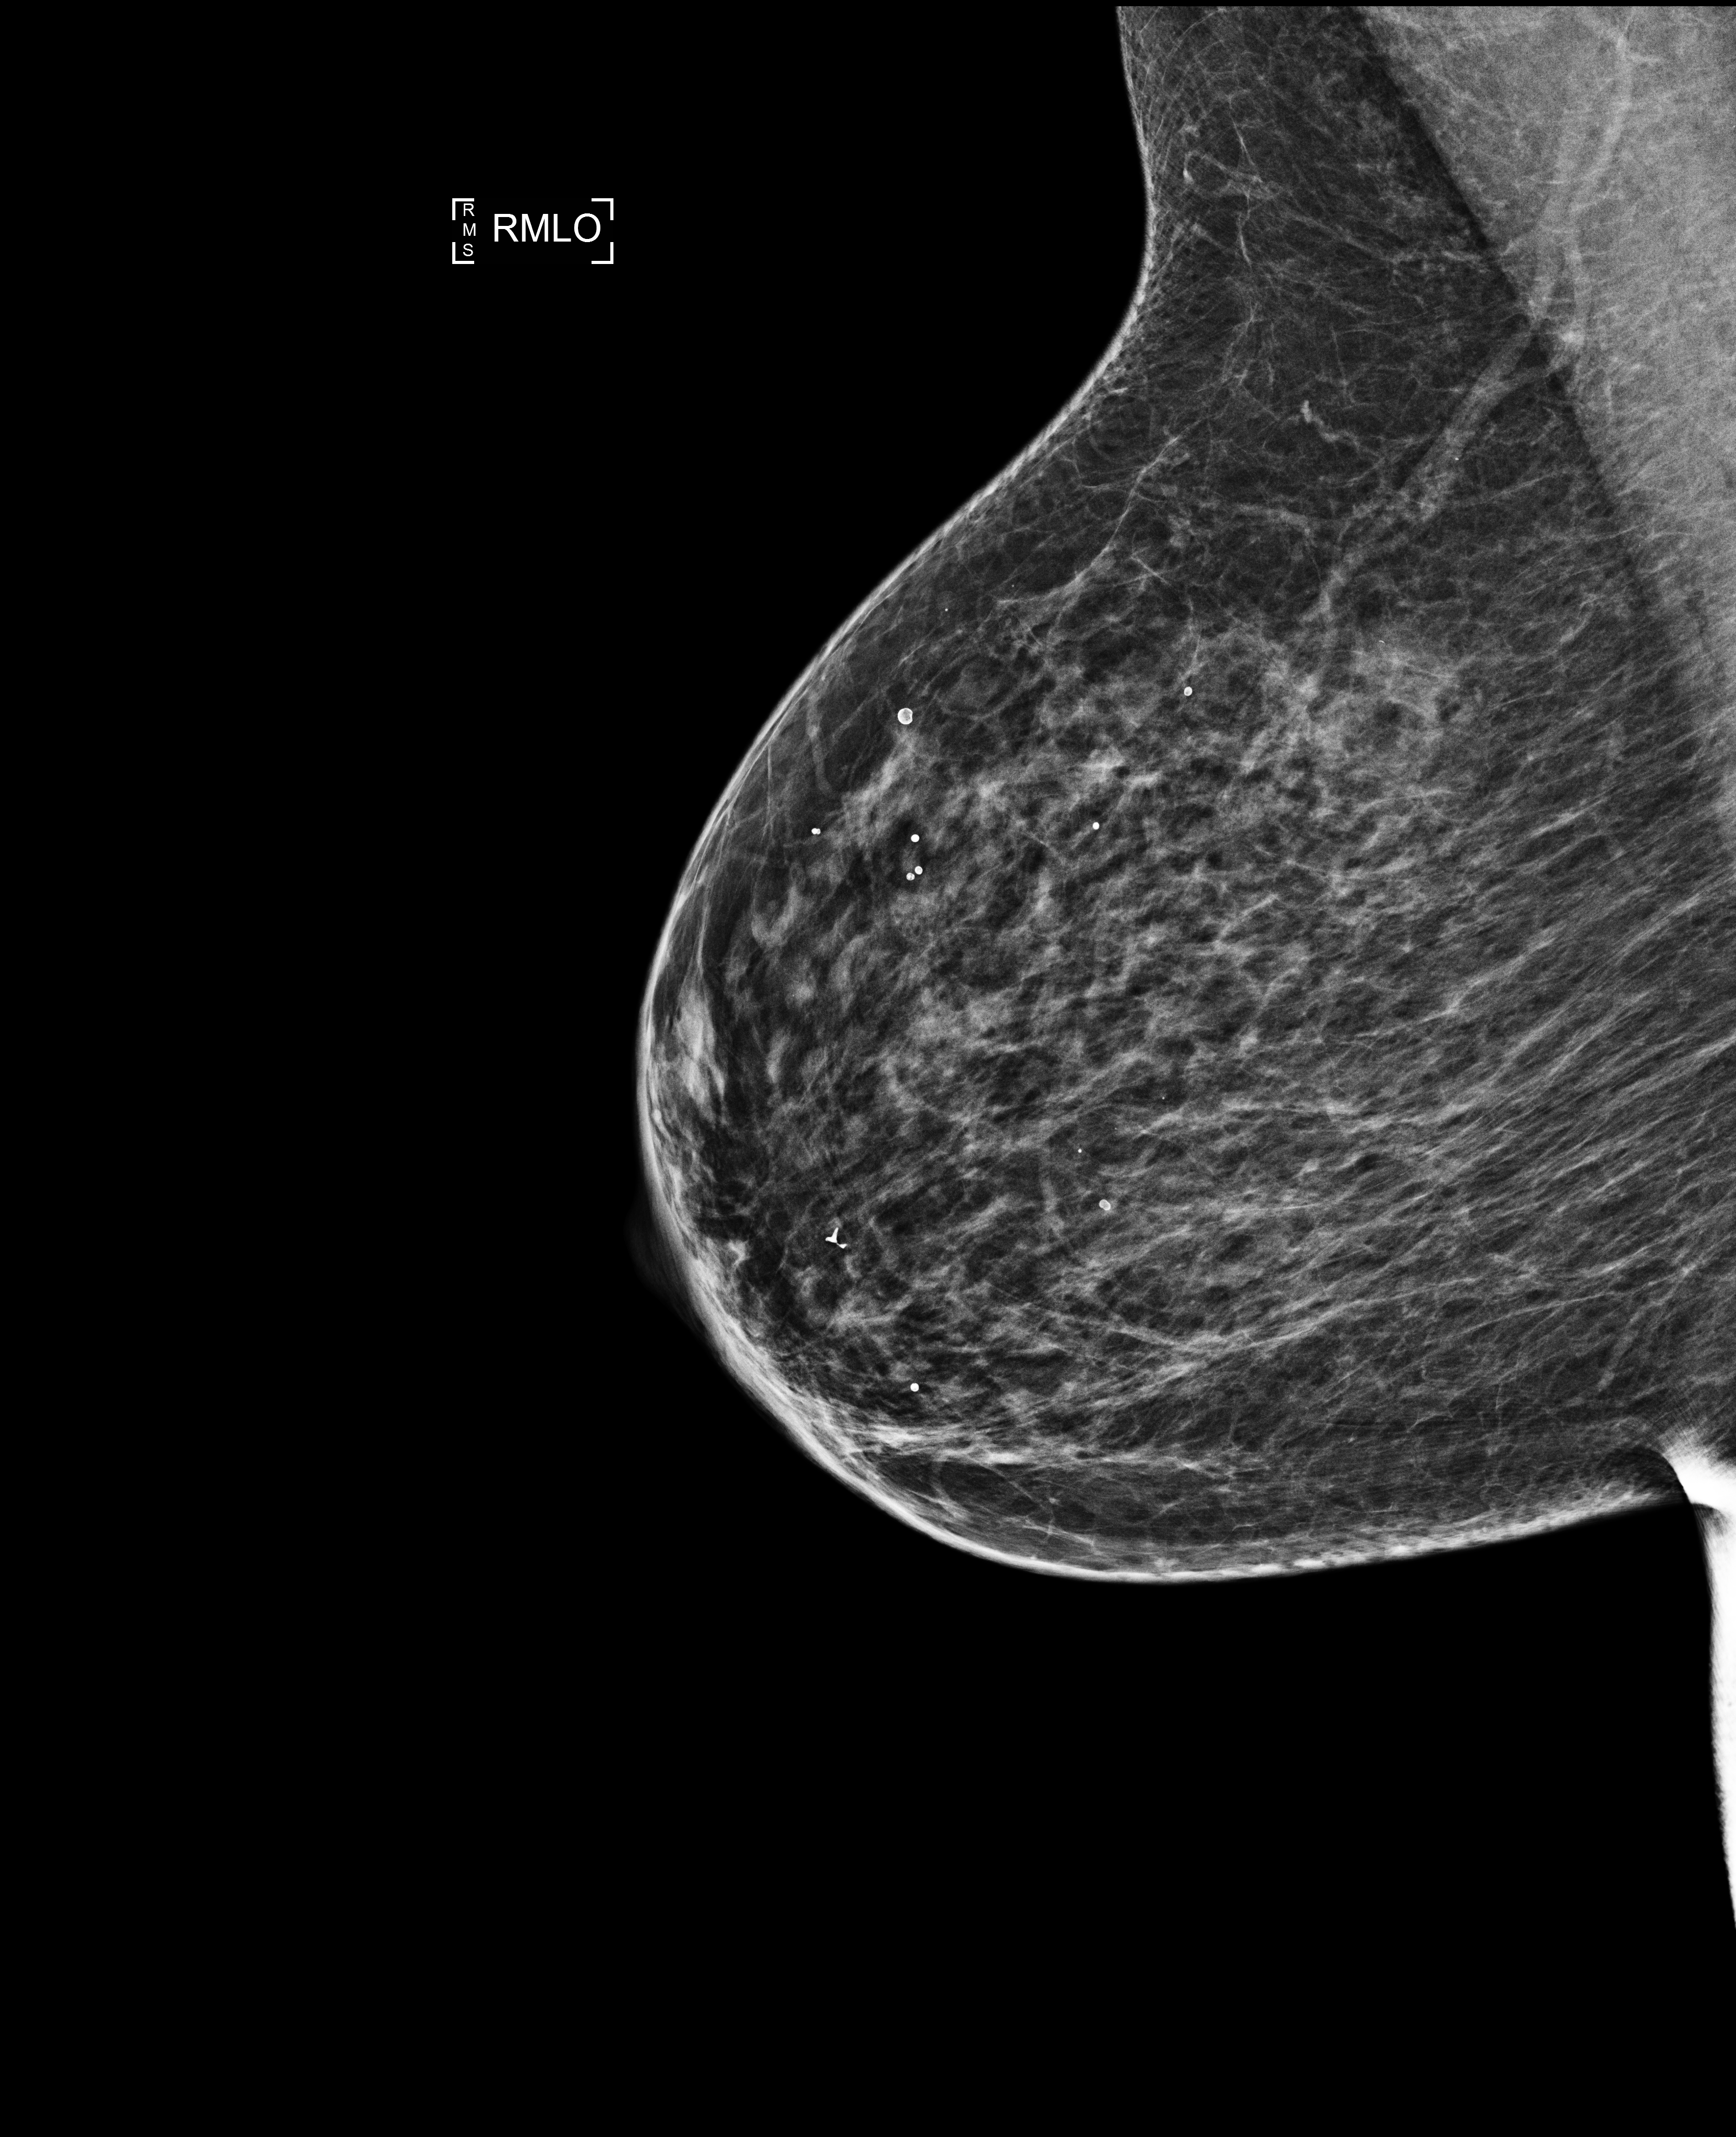
Screening examination. Patient: female, 68 years.
Image type: full-field digital mammogram. Breast: right. Projection: MLO view. BI-RADS breast density category at the screening exam (both breasts, scale 1–4): 3. Final BI-RADS assessment for this screening round (tomosynthesis exam, both breasts): category 1. Recall: no recall after this screen.